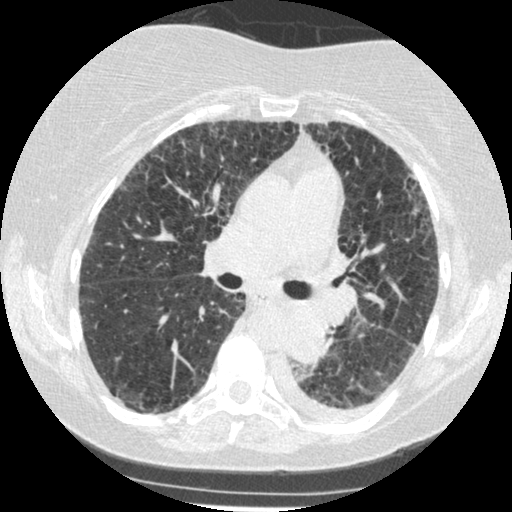
Low-dose screening chest CT, one axial slice. Position 153 of 341 along the scan axis. Reconstruction kernel STANDARD. 120 kVp. Lung window (W 1500 / L -600 HU). 1.25 mm slice thickness. 512 × 512 image matrix, field of view 310 × 310 mm.
Structures marked on this image (expert manual segmentation):
- lesion 1 (tumor, lower lobe of left lung): bounding box (x1, y1, x2, y2) in pixels: (287, 308, 330, 364)